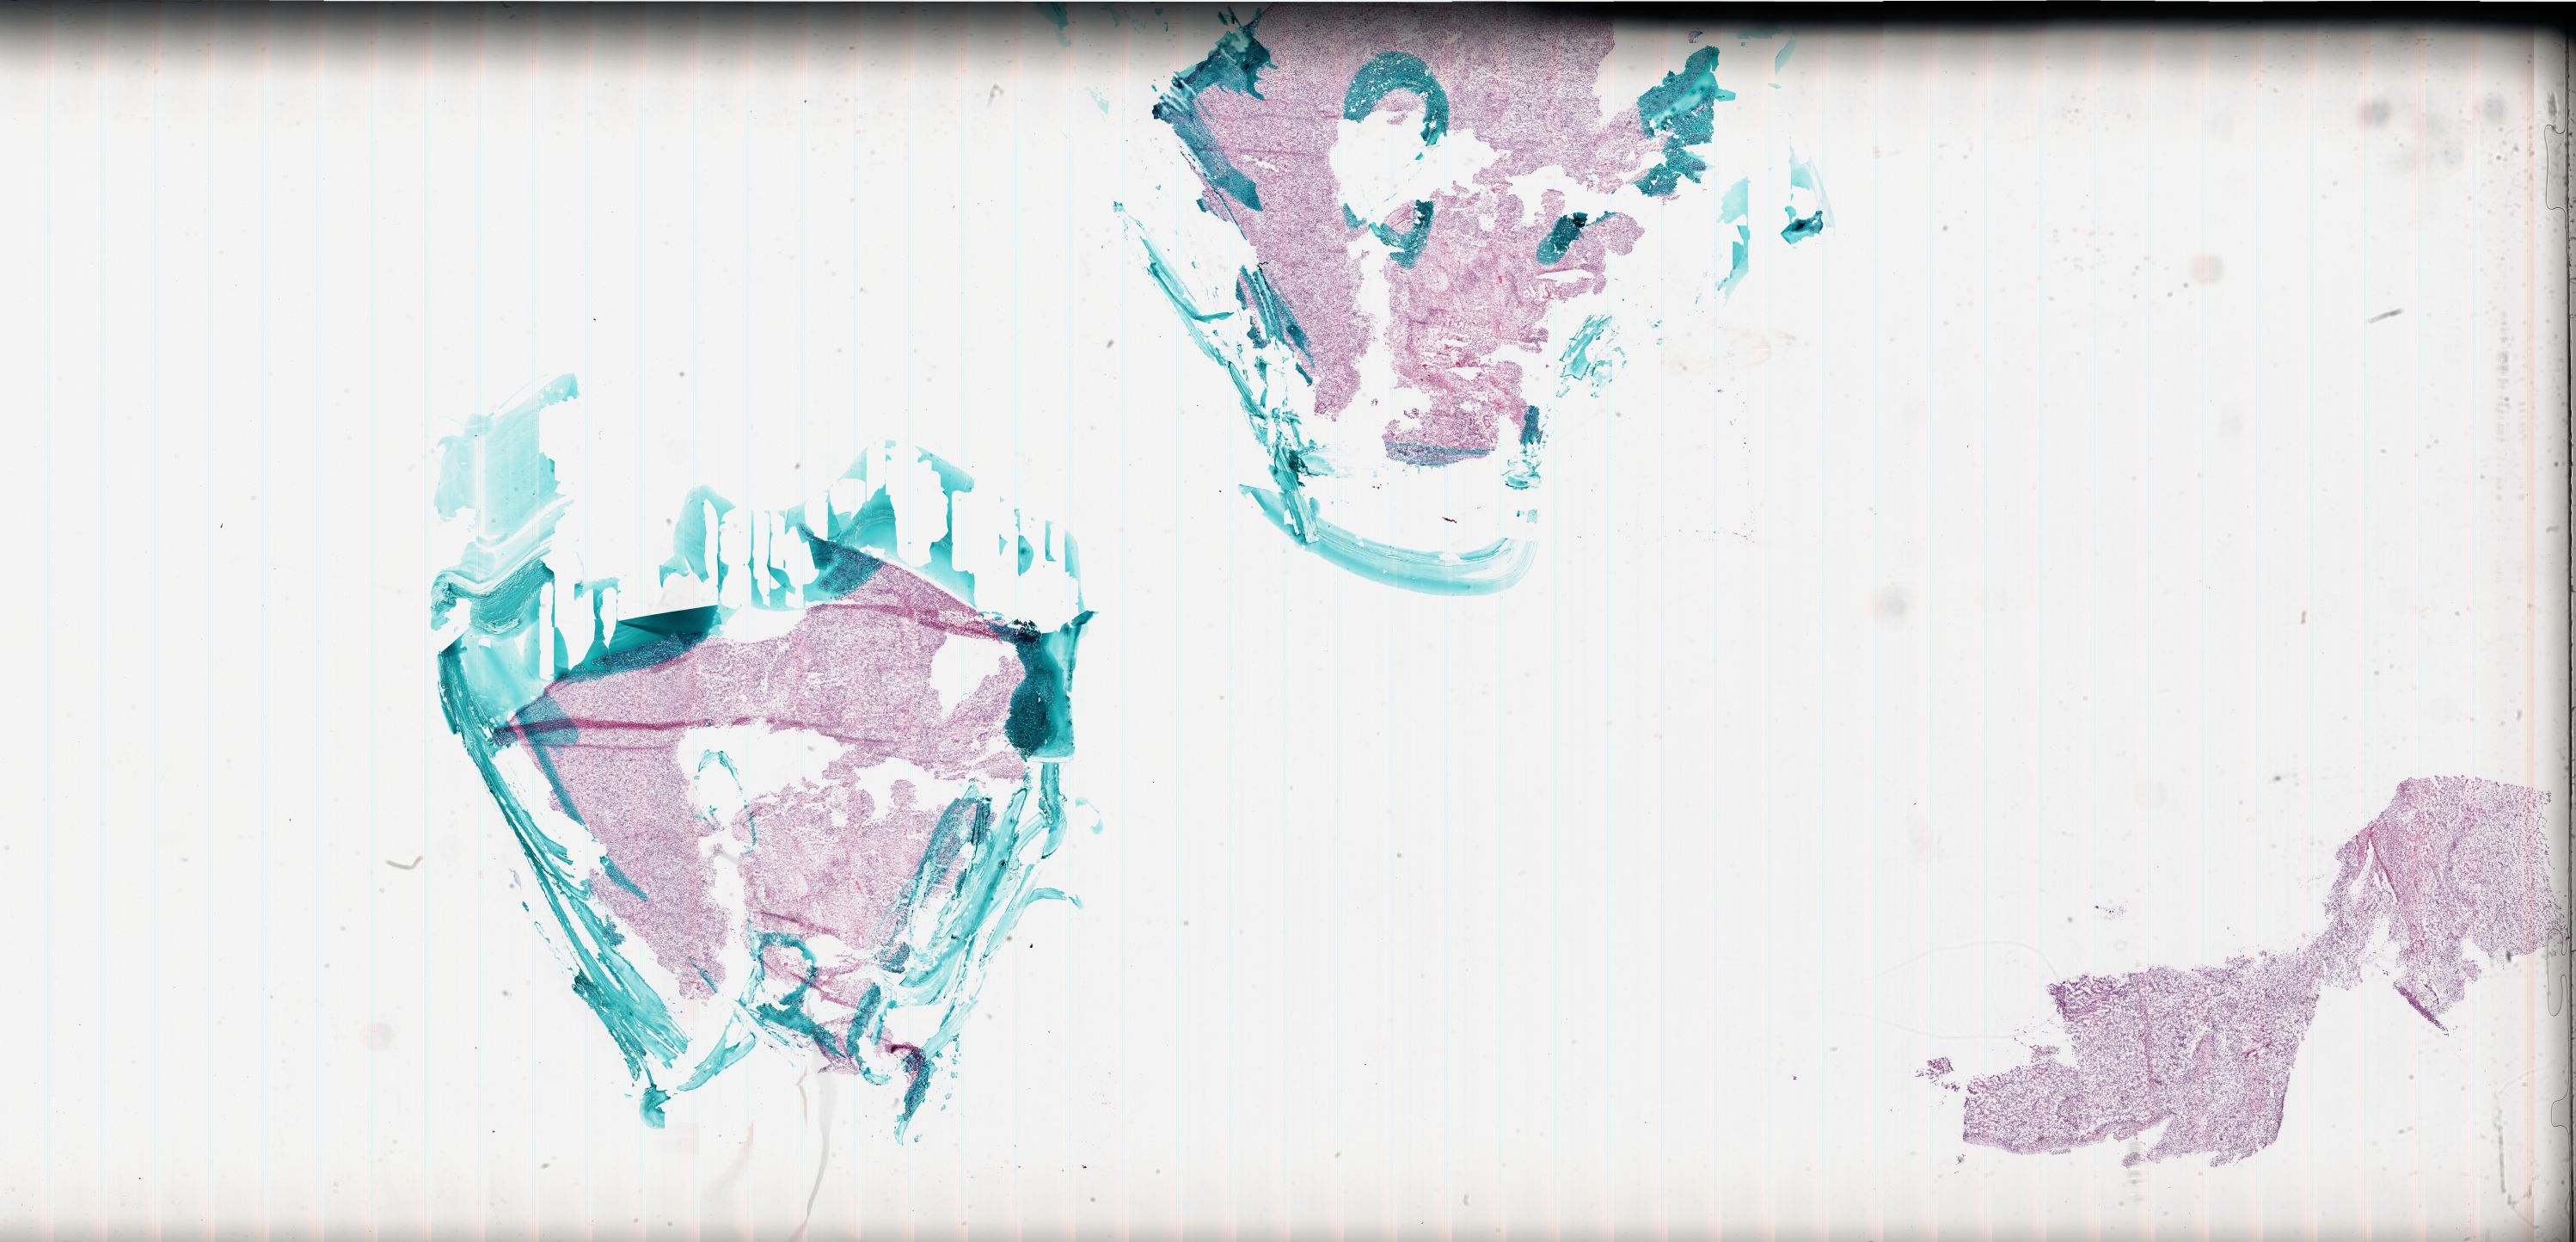
Digitized Hematoxylin and eosin (H&E) stained tissue section (whole slide), shown as a low-resolution overview of the whole scanned area (about 48.0 x 23.1 mm). Frozen section from the bottom of the tissue portion. Brain, primary tumour sample. Patient: female, age at initial diagnosis 45 years. Composition of this section per pathologist review: tumour cells 80%, tumour nuclei 100%, normal cells 0%, stromal cells 0%, necrosis 20%.
Histologic diagnosis: Glioblastoma.